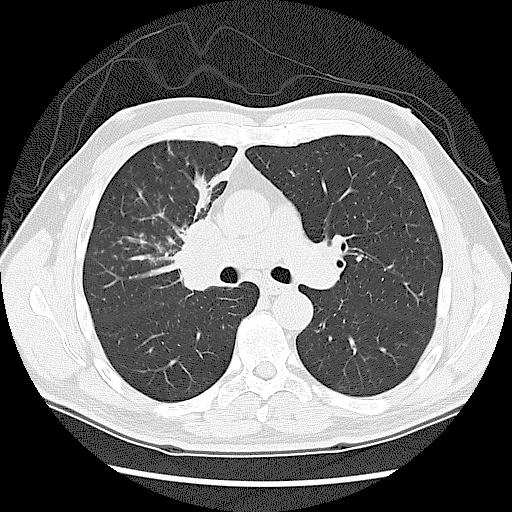
Axial slice from a low-dose chest CT screening exam; baseline screening round; lung window (W 1500 / L -600 HU); slice 55 of 131 in the series; 512 × 512 image matrix, field of view 360 × 360 mm. Male, age 60 years at enrolment. Current smoker at enrolment.
- Expert reader's lesion annotation, bounding box (x1, y1, x2, y2) in pixels: (158, 219, 241, 311).
- No non-calcified nodule or mass ≥4 mm was recorded by the screening reader at this exam.
- Participant outcome: lung cancer diagnosed 41 days after this screen — small cell carcinoma, NOS, right upper lobe, stage IIIA (AJCC 6th edition).